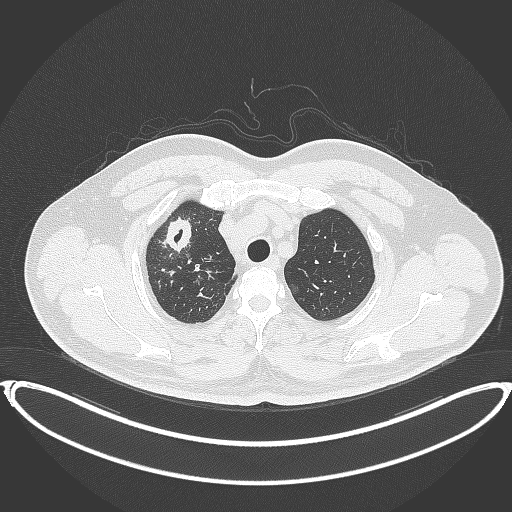
Chest CT, one axial slice. Position 327 of 399 along the scan axis. Reconstruction kernel B70f. 120 kVp. Lung window (W 1500 / L -600 HU). 1 mm slice thickness. 512 × 512 image matrix. Patient: male, 53 years. Case-level facts recorded for this patient, not image findings: clinical TNM (as recorded): T2a N0 M0.
Outlined on this slice (bounding box drawn by a radiologist):
- lung tumour (recorded histology: adenocarcinoma): bounding box (x1, y1, x2, y2) in pixels: (156, 211, 195, 258)